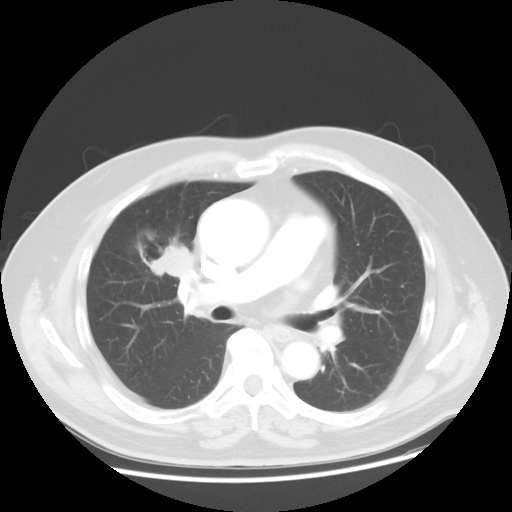
Chest CT, one axial slice. 120 kVp. Lung window (W 1500 / L -600 HU). 5 mm slice thickness. 512 × 512 image matrix, field of view 392 × 392 mm. Patient: male, 60 years. Case-level facts recorded for this patient, not image findings: clinical TNM (as recorded): T2 N3 M0; histopathological grade: G2-3.
Outlined on this slice (rectangle marked by the reading radiologist):
- lung tumour (recorded histology: adenocarcinoma): bounding box <134,228,189,285> (left, top, right, bottom; pixels)